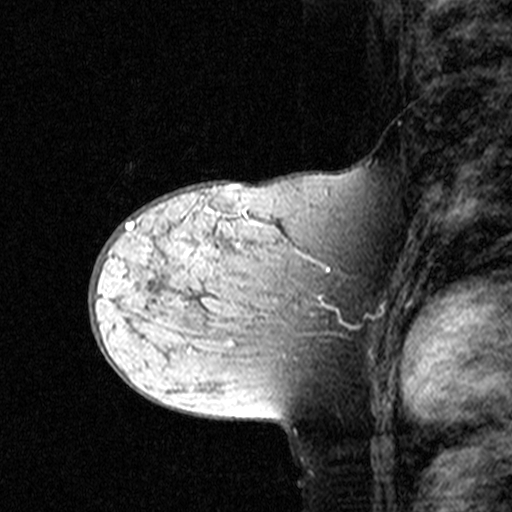
Breast MRI (dynamic contrast-enhanced), one sagittal slice; position 22 of 44 along the scan axis; dynamic contrast-enhanced study with each time point stored as its own series, time point 2 of 3 at this slice position (early post-contrast, ordered by acquisition time); 1.5 T; TE 4.5 ms, TR 11 ms; 512 × 512 image matrix. Female patient, age 44 years. From the clinical record (not read from this slice): setting: breast cancer imaged before/during neoadjuvant chemotherapy; receptor status: triple-negative.
Structures marked on this image (semi-automatically segmented with operator editing):
- analysis volume of interest (the breast-tissue region the enhancement analysis was run in; not a lesion): bounding box [x1, y1, x2, y2] px = [142, 208, 349, 363]
- tumour enhancement mask (voxels above the 90 % enhancement threshold inside the analysis volume of interest): [192, 211, 339, 316]